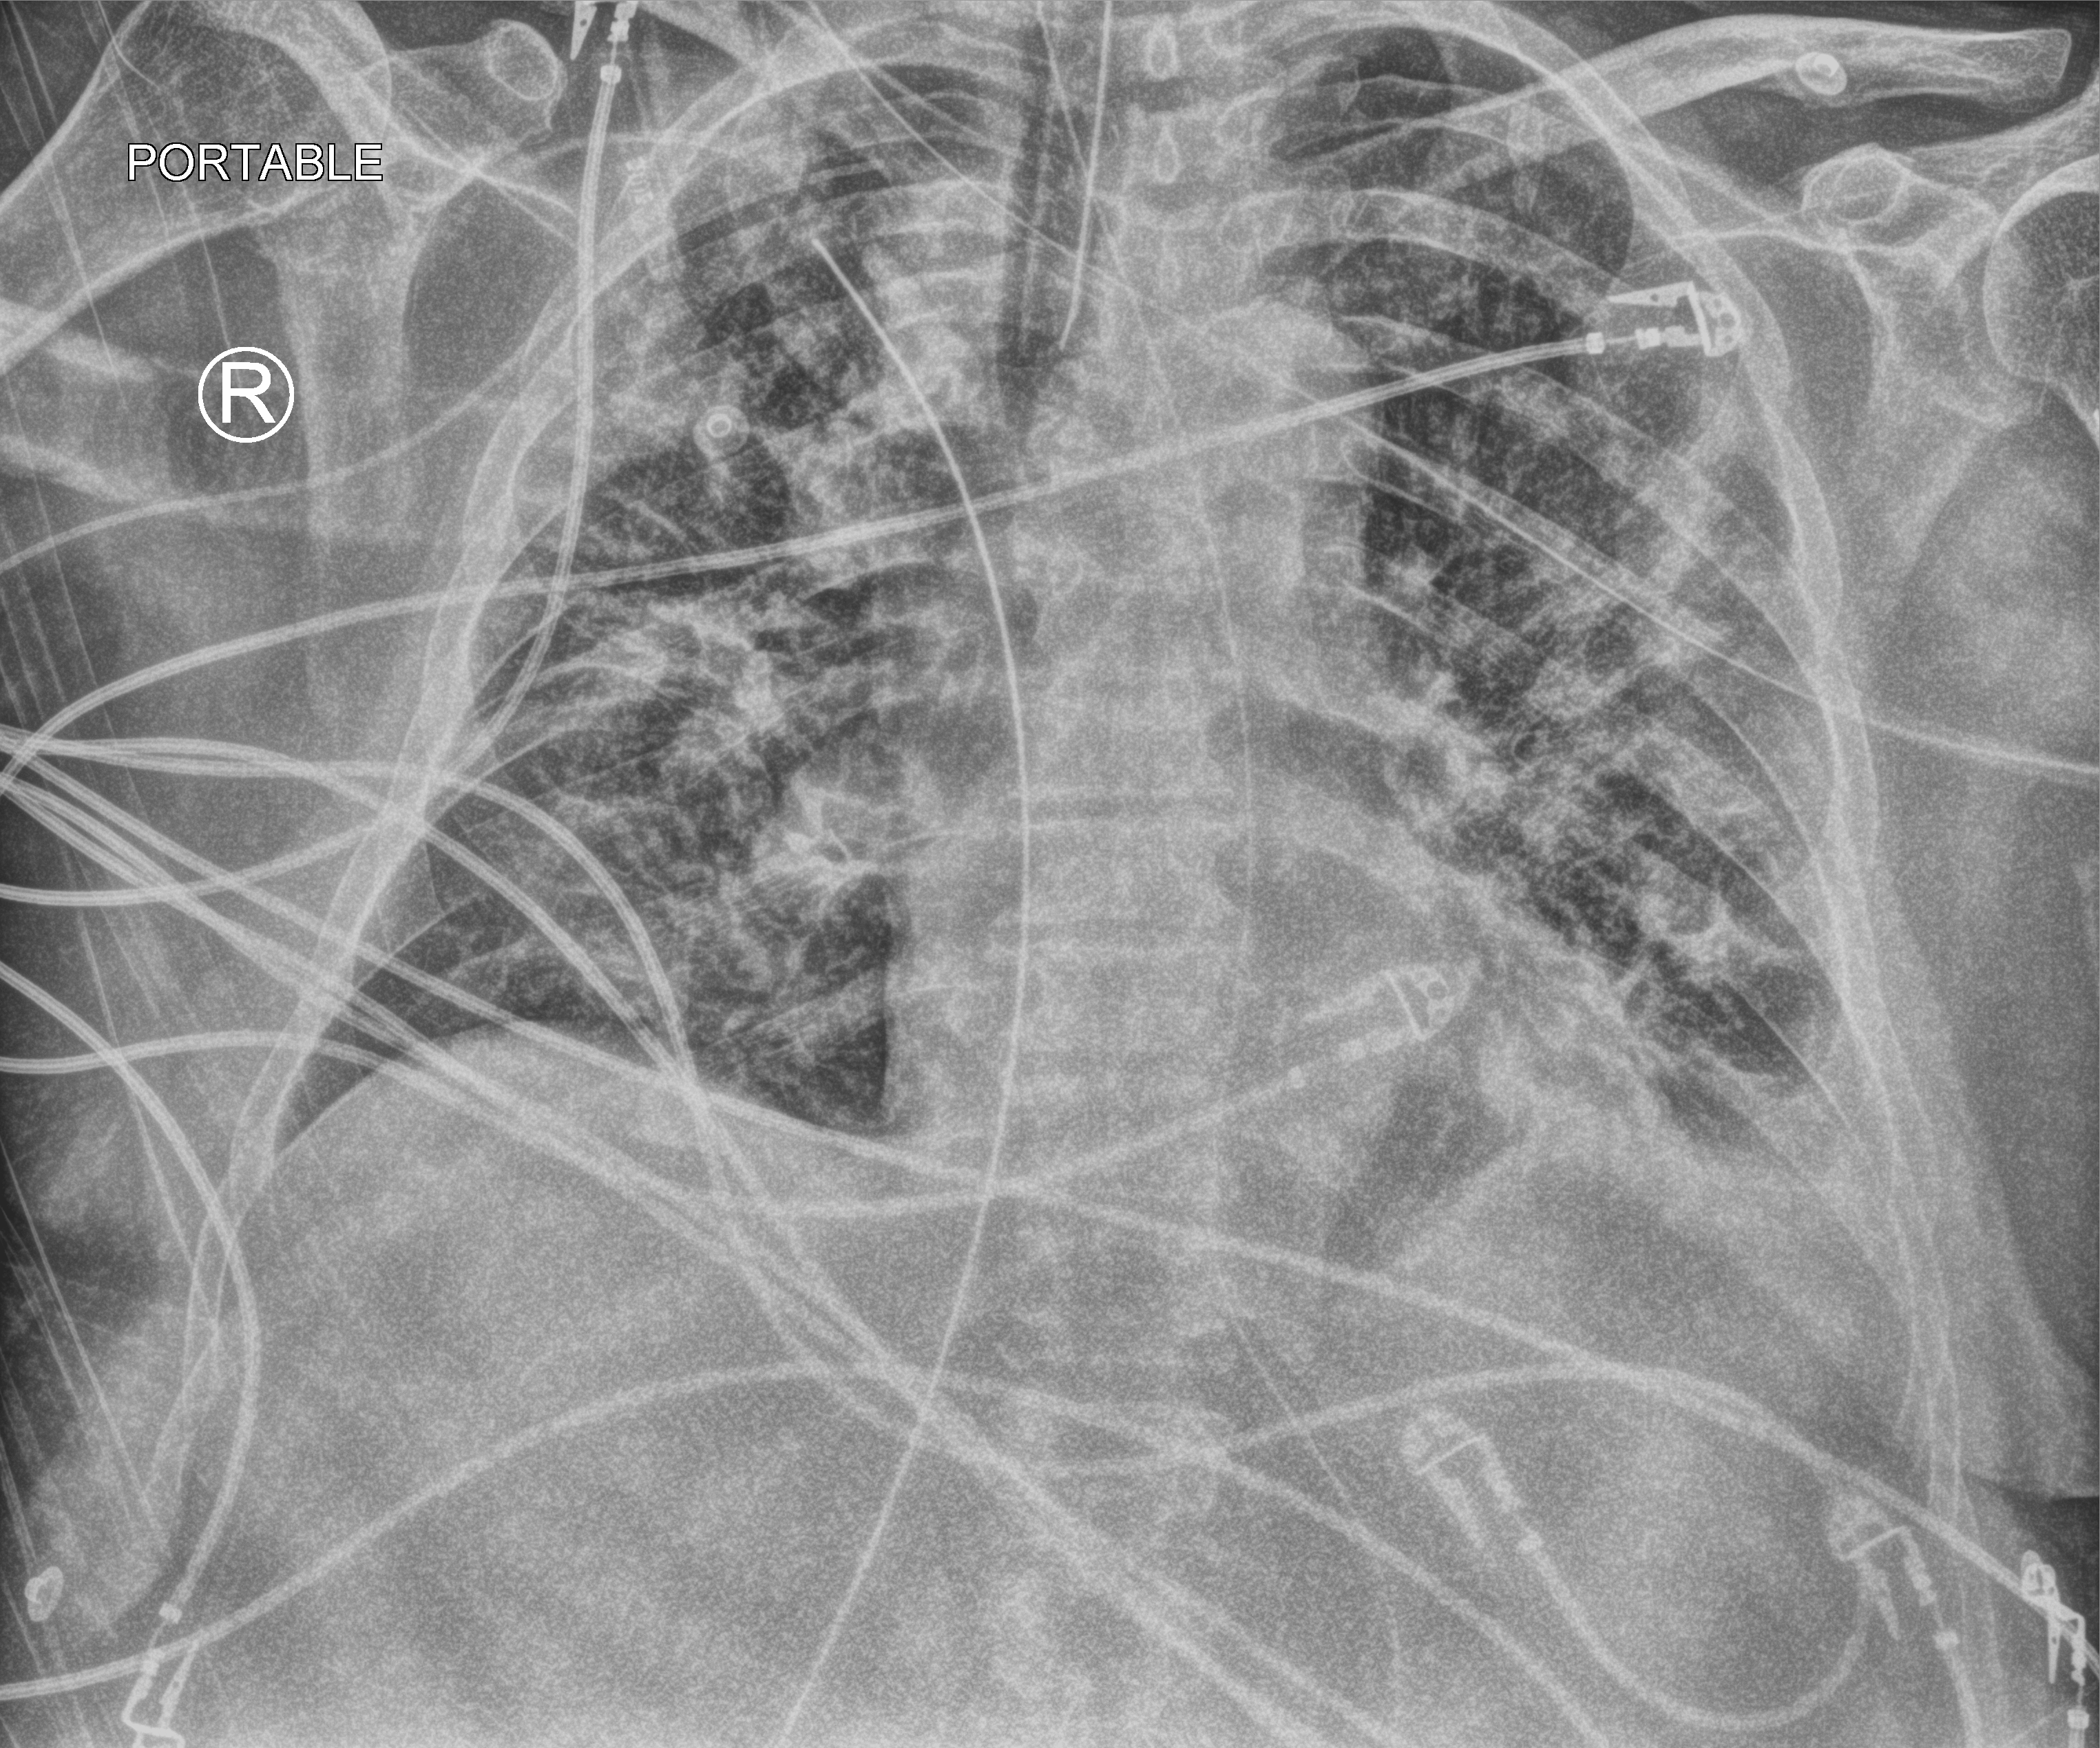
Portable chest radiograph; anteroposterior (AP) projection. Male patient hospitalised with COVID-19, age 60–74 years.
Hospital-stay facts (about this admission, not read from this image; timing relative to this image not recorded):
- mechanically ventilated during this hospital stay: yes